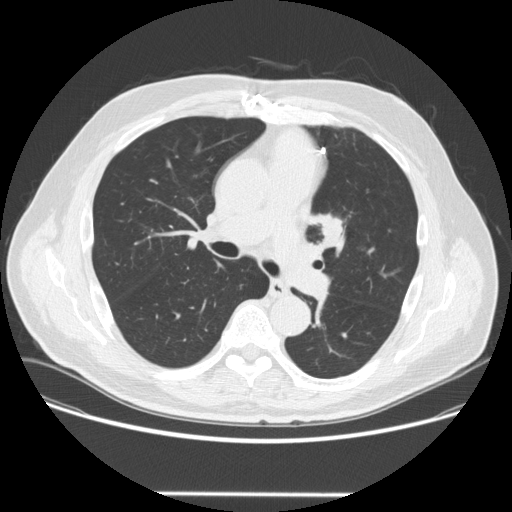
Axial slice from a low-dose chest CT screening exam, third annual screen, lung window (W 1500 / L -600 HU), standard (soft-tissue) reconstruction kernel (STANDARD), 120 kVp. Male participant, aged 66 years at enrolment. Former smoker at enrolment.
Expert-annotated lung lesion, box from (x=305, y=207) to (x=357, y=255) px. The screening reader recorded 2 non-calcified nodules or masses ≥4 mm on this exam (left upper lobe, right lower lobe); which of them this box marks is not recorded. Official screen result: positive, other. Lung cancer was diagnosed 85 days after this screen: squamous cell carcinoma, NOS, left upper lobe, poorly differentiated (G3), stage IA (AJCC 6th edition), 27 mm at pathology.